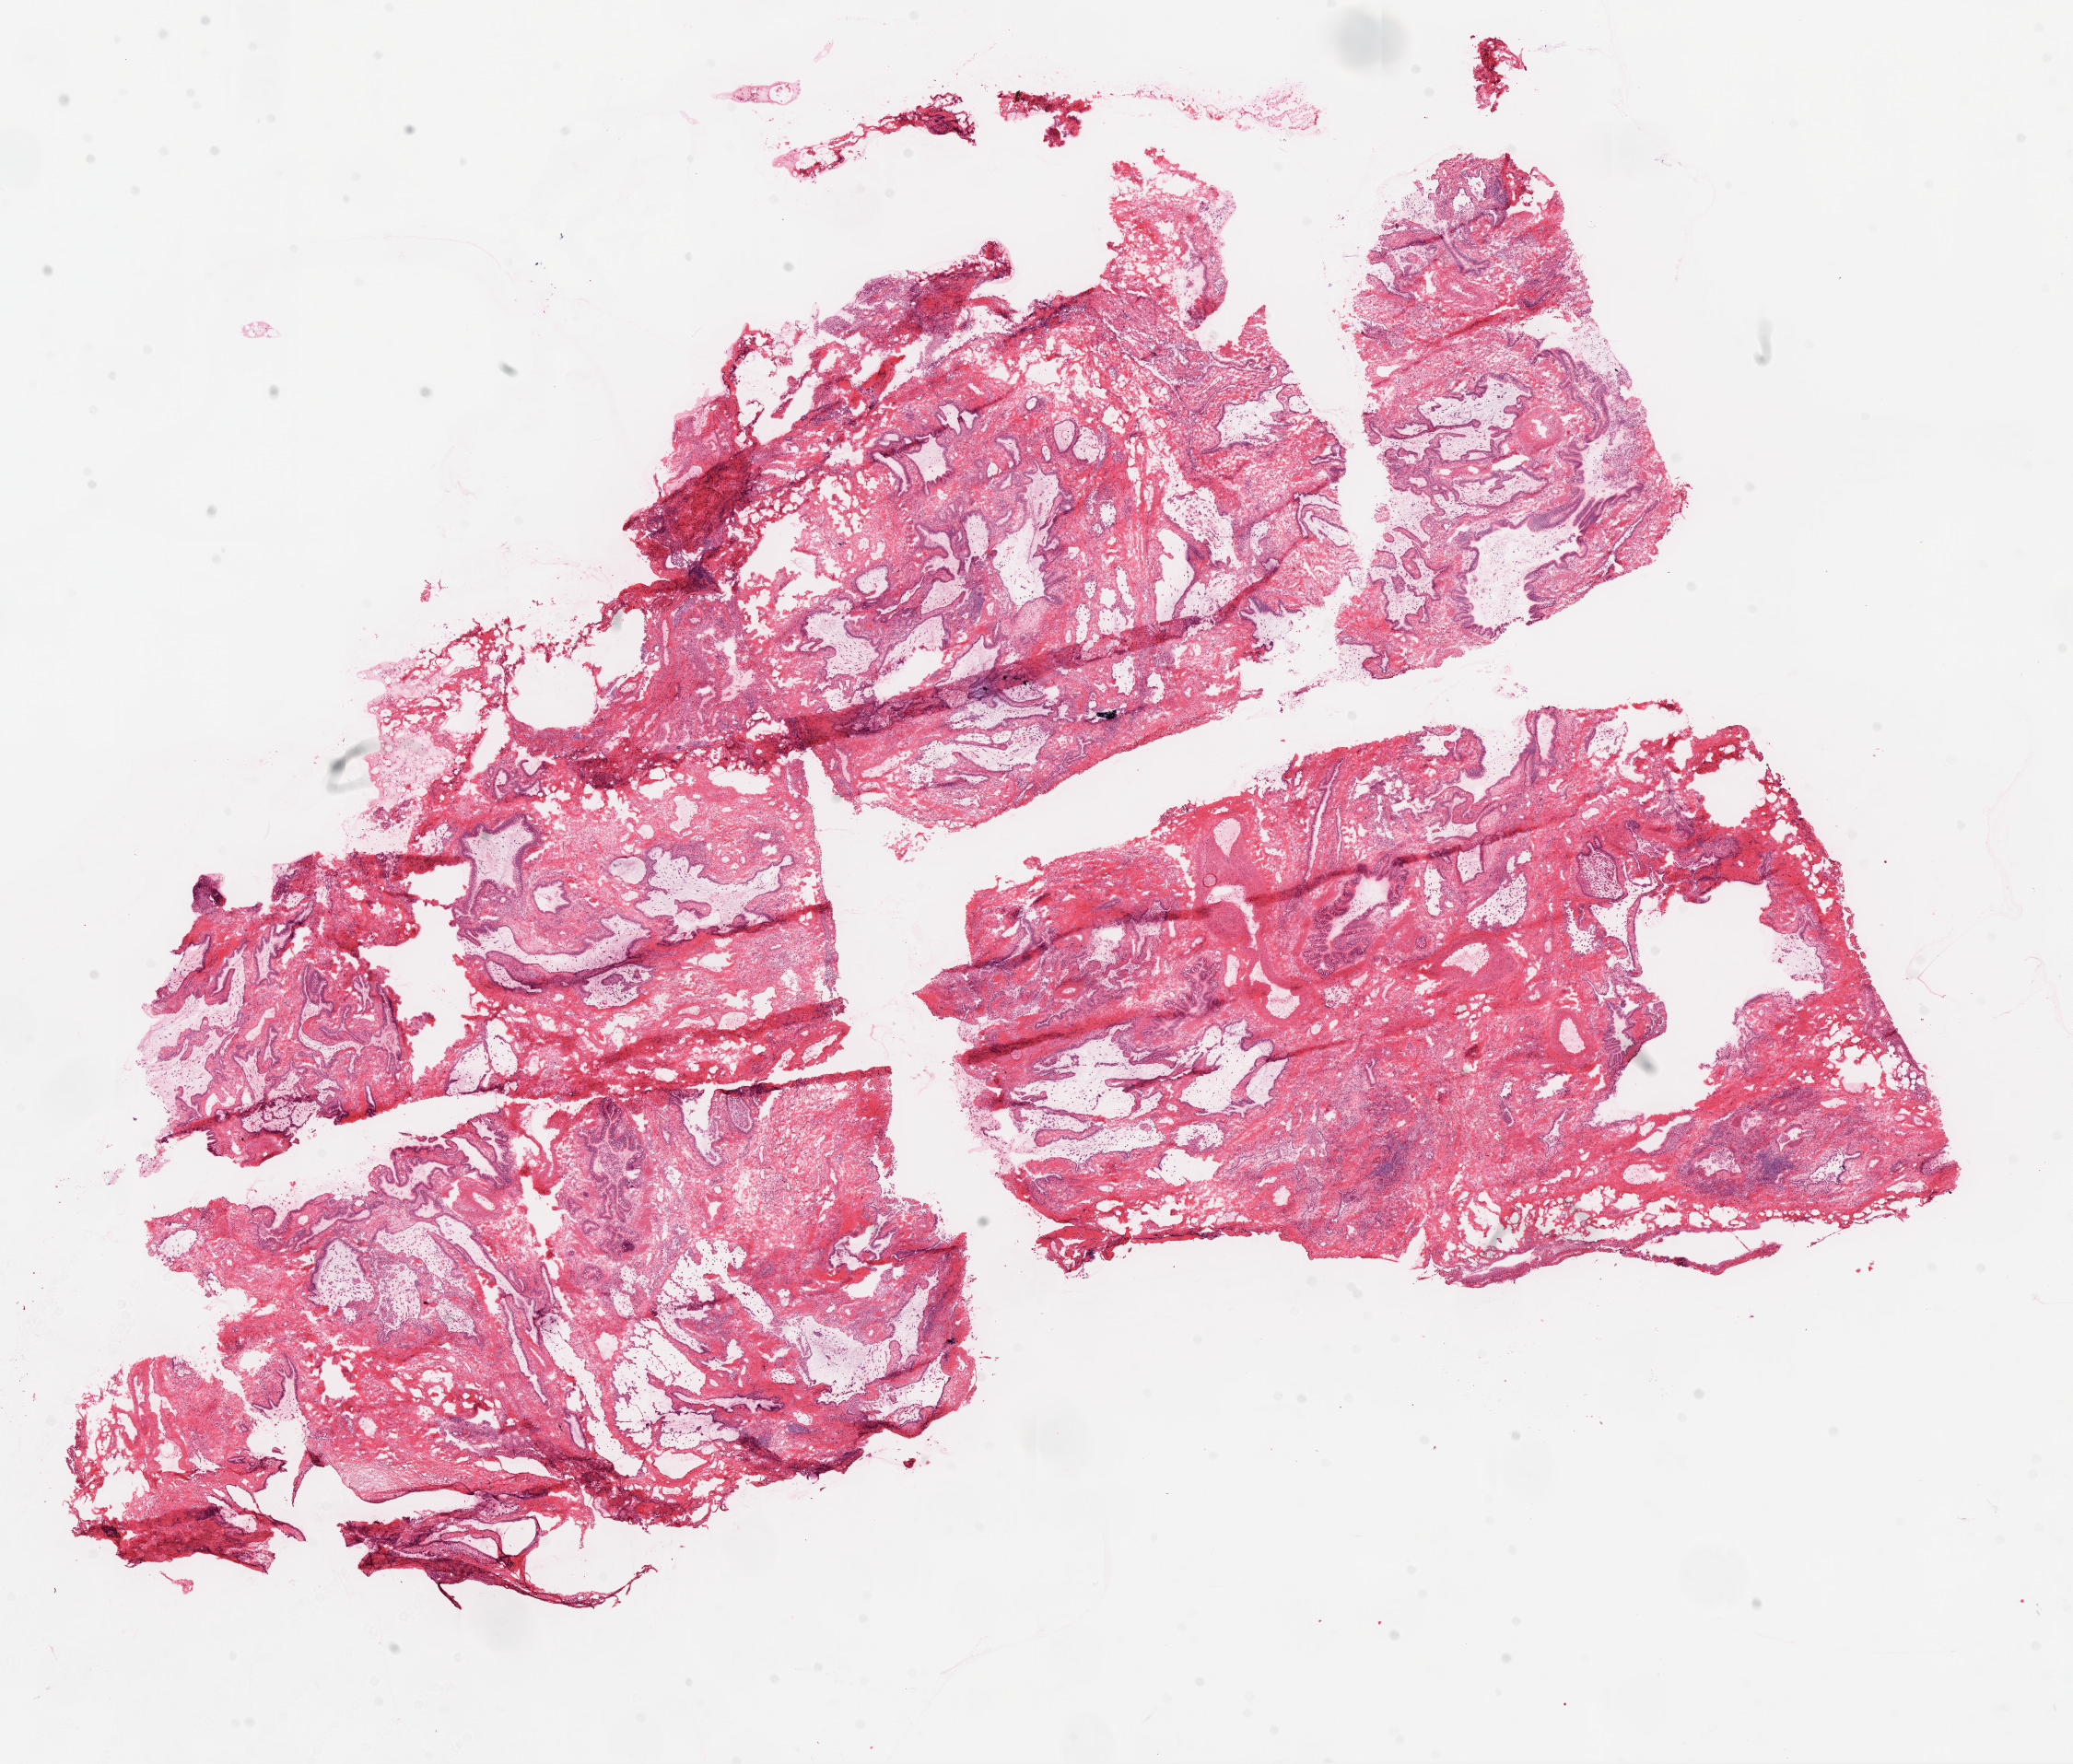
Whole-slide histology image, H&E-stained — a low-resolution overview of the entire scanned area, about 18.1 x 15.4 mm, frozen section from the top of the tissue portion, lung, solid tissue normal (non-tumour tissue) sample. Male, age 75 years at initial diagnosis.
This section: solid tissue normal sample (biorepository sample class). Patient diagnosis: Squamous cell carcinoma, NOS (upper lobe, lung).